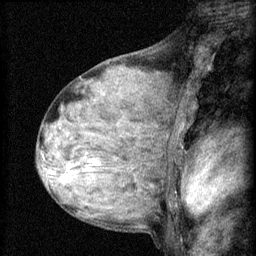
Breast MRI (dynamic contrast-enhanced), one sagittal slice. Position 38 of 60 along the scan axis. 3 images stored at this slice position (order not interpretable as contrast timing). 1.5 T. TE 4.2 ms, TR 8.2 ms. 2 mm slice thickness. 256 × 256 image matrix, field of view 180 × 180 mm. Female patient, age 48 years.
Outlined on this slice (semi-automatically segmented with operator editing):
- analysis volume of interest (the breast-tissue region the enhancement analysis was run in; not a lesion): bounding box (x1, y1, x2, y2) in pixels: (54, 138, 133, 191)
- tumour enhancement mask (voxels above the 70 % enhancement threshold inside the analysis volume of interest): (54, 160, 97, 175)